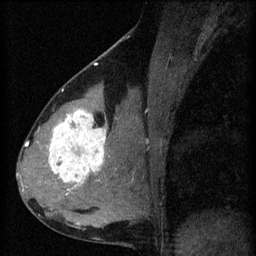
Breast MRI (dynamic contrast-enhanced), one sagittal slice. Position 33 of 60 along the scan axis. 3 images stored at this slice position (order not interpretable as contrast timing). 1.5 T. TE 4.2 ms, TR 8.2 ms. 256 × 256 image matrix. Female patient, age 37 years.
Annotated regions visible in this slice (semi-automatically segmented with operator editing):
- analysis volume of interest (the breast-tissue region the enhancement analysis was run in; not a lesion): bounding box <44,100,119,197> (left, top, right, bottom; pixels)
- tumour enhancement mask (voxels above the 70 % enhancement threshold inside the analysis volume of interest): <48,110,108,191>